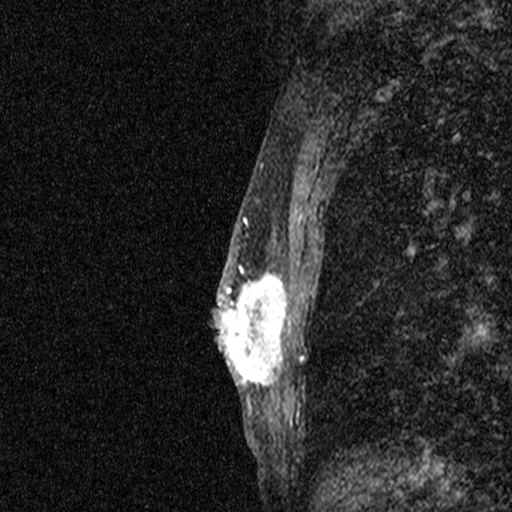
Breast MRI (dynamic contrast-enhanced), one sagittal slice. Slice 26 of 44 in the series (ordered by position). Dynamic contrast-enhanced study with each time point stored as its own series, time point 2 of 3 at this slice position (early post-contrast, ordered by acquisition time). 1.5 T. TE 4.5 ms, TR 11 ms. 2.05 mm slice thickness. 512 × 512 image matrix, field of view 200 × 200 mm. Patient: female, 44 years. From the clinical record (not read from this slice): setting: breast cancer imaged before/during neoadjuvant chemotherapy; receptor status: HR-positive, HER2-negative.
Structures marked on this image (semi-automatically segmented with operator editing):
- analysis volume of interest (the breast-tissue region the enhancement analysis was run in; not a lesion): bounding box [x1, y1, x2, y2] px = [204, 254, 287, 401]
- tumour enhancement mask (voxels above the 90 % enhancement threshold inside the analysis volume of interest): [217, 265, 285, 398]